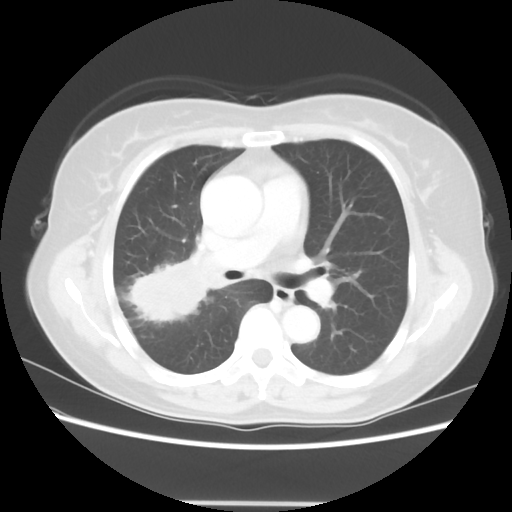
Chest CT, one axial slice; slice 35 of 56 in the series (ordered by position); reconstruction kernel STANDARD; lung window (W 1500 / L -600 HU); 5 mm slice thickness; 512 × 512 image matrix, field of view 360 × 360 mm. Female patient, age 55 years. From the clinical record (not read from this slice): clinical TNM (as recorded): T2 N1 M0.
Outlined on this slice (rectangle marked by the reading radiologist):
- lung tumour (recorded histology: adenocarcinoma): bounding box (x1, y1, x2, y2) in pixels: (123, 249, 225, 330)